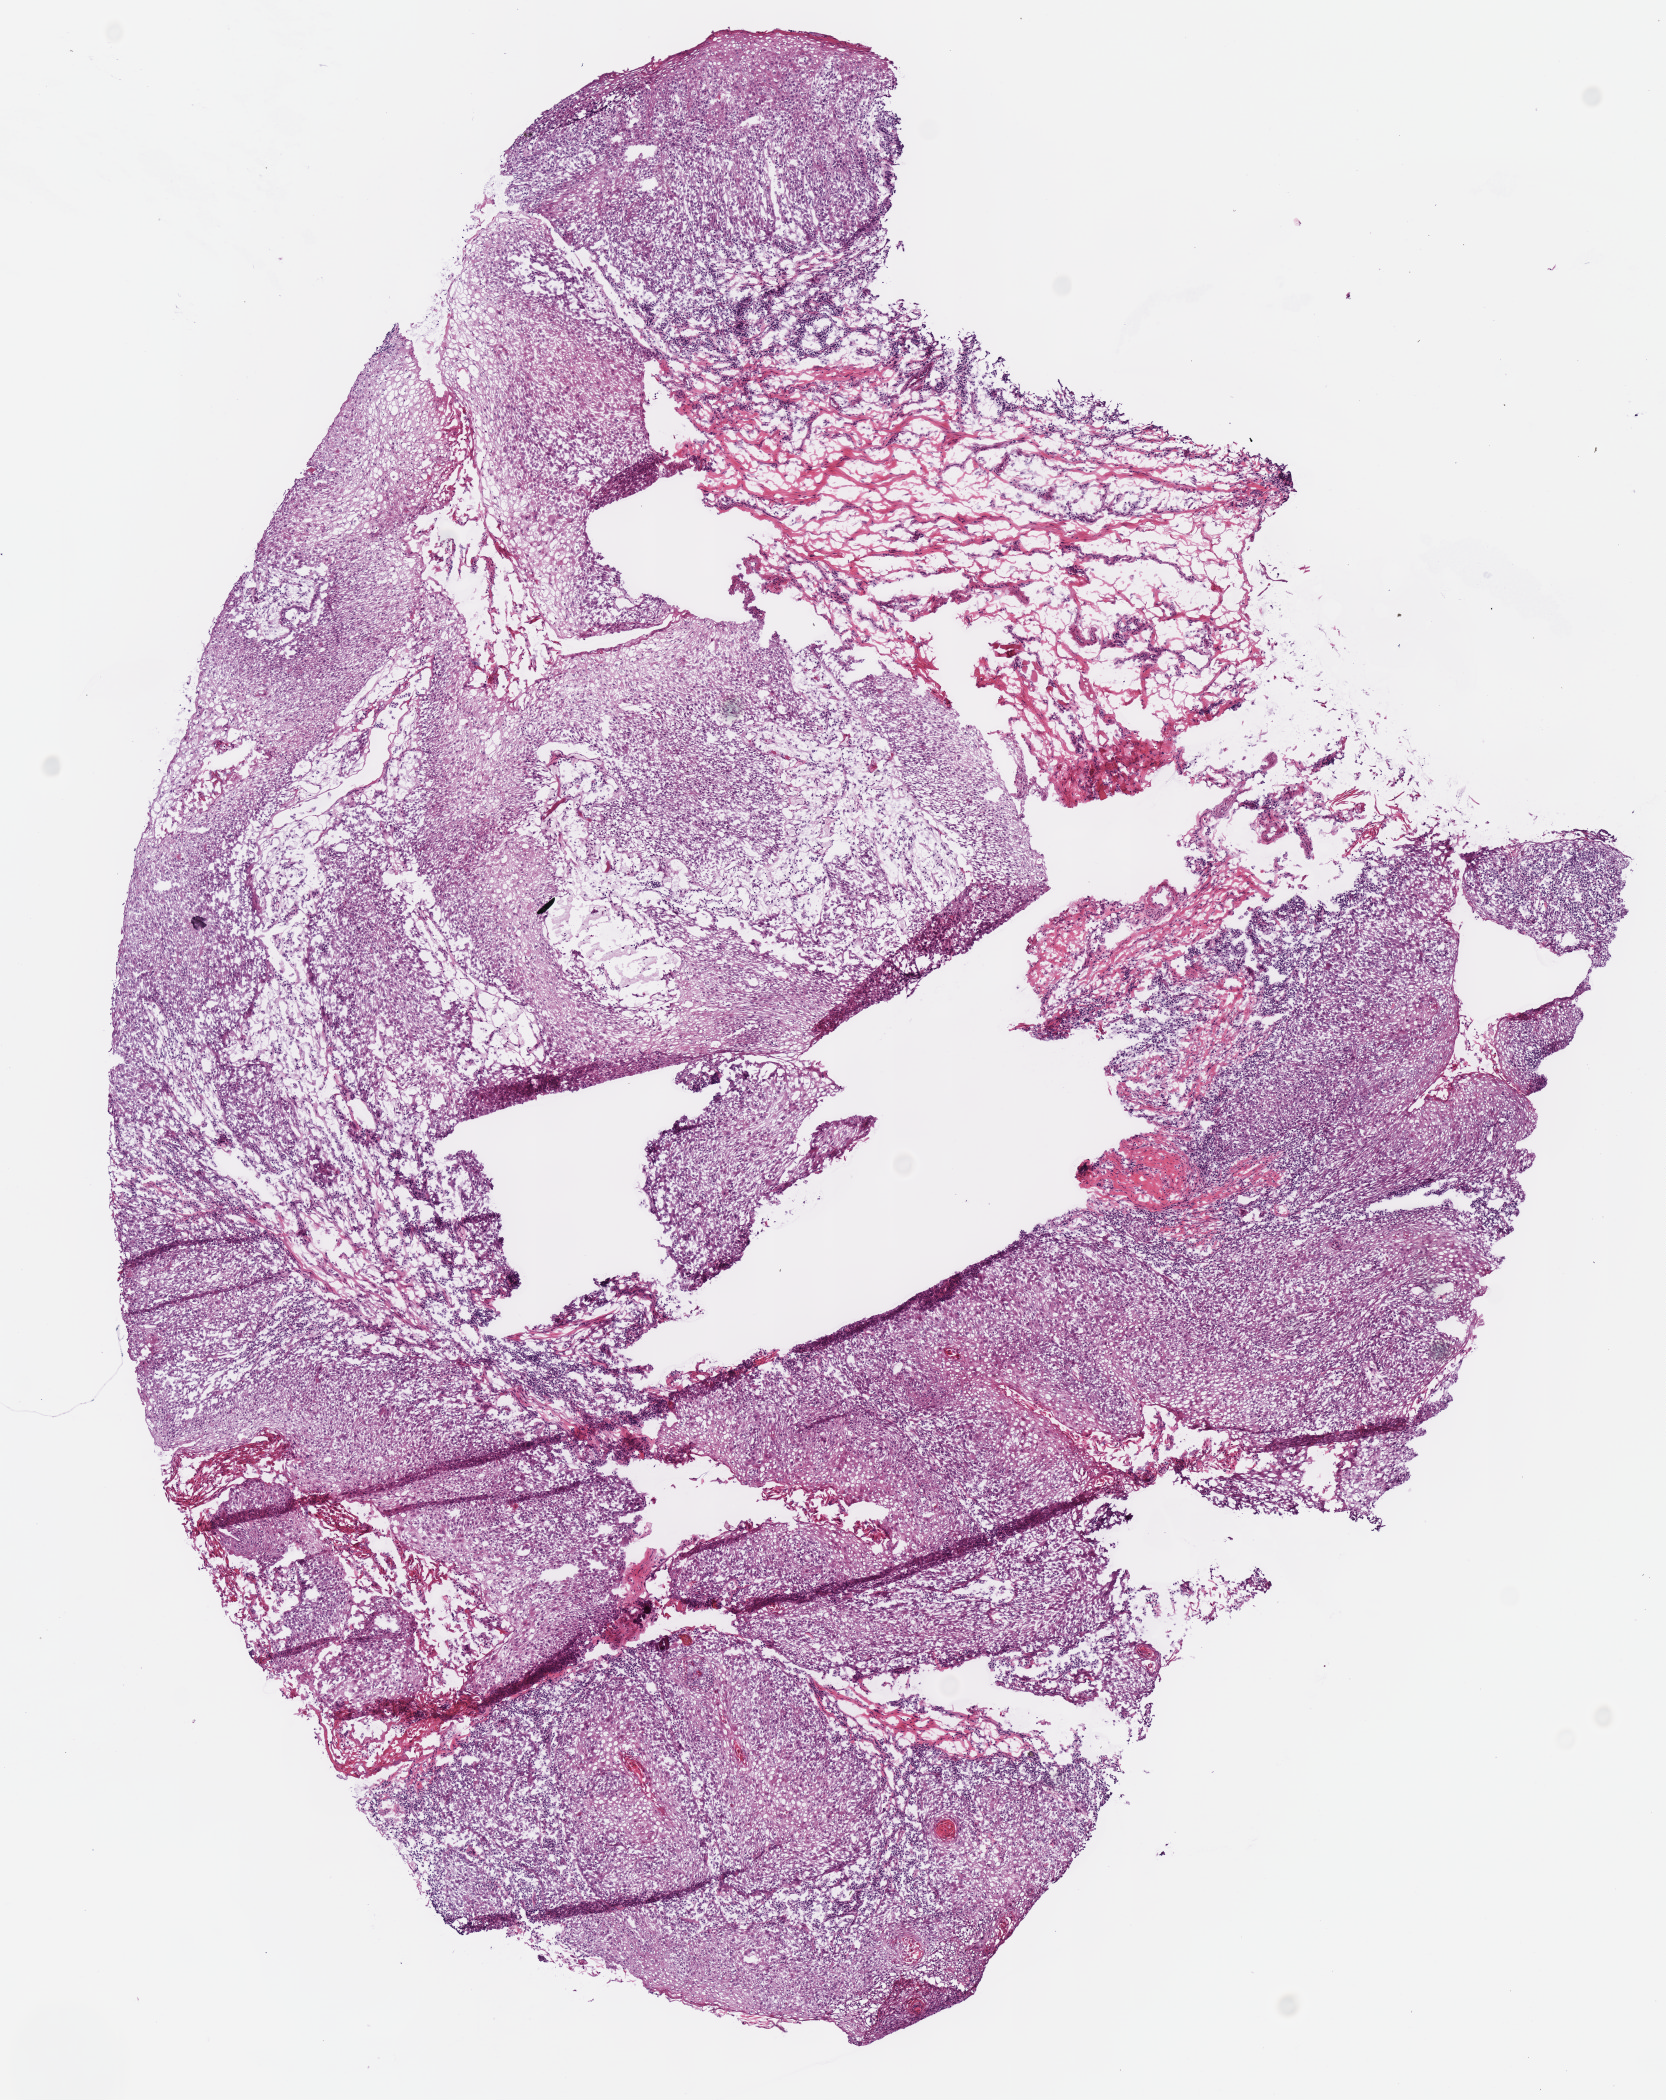
Whole-slide histology image, H&E-stained, shown as a low-resolution overview of the whole scanned area (about 6.6 x 8.3 mm), frozen section from the top of the tissue portion, sample: primary tumour, head and neck. Female patient; age at initial diagnosis 73 years. Histologic grade: G1 (well differentiated). Pathologist review of this section (percent, as recorded): tumour cells 95%, tumour nuclei 80%, normal cells 0%, stromal cells 5%, necrosis 0%. Inflammatory infiltration, as recorded: lymphocyte infiltration 15%, monocyte infiltration 0%, neutrophil infiltration 0%.
Histologic diagnosis: Squamous cell carcinoma, NOS. AJCC pathologic stage: II. TNM: T2 NX.